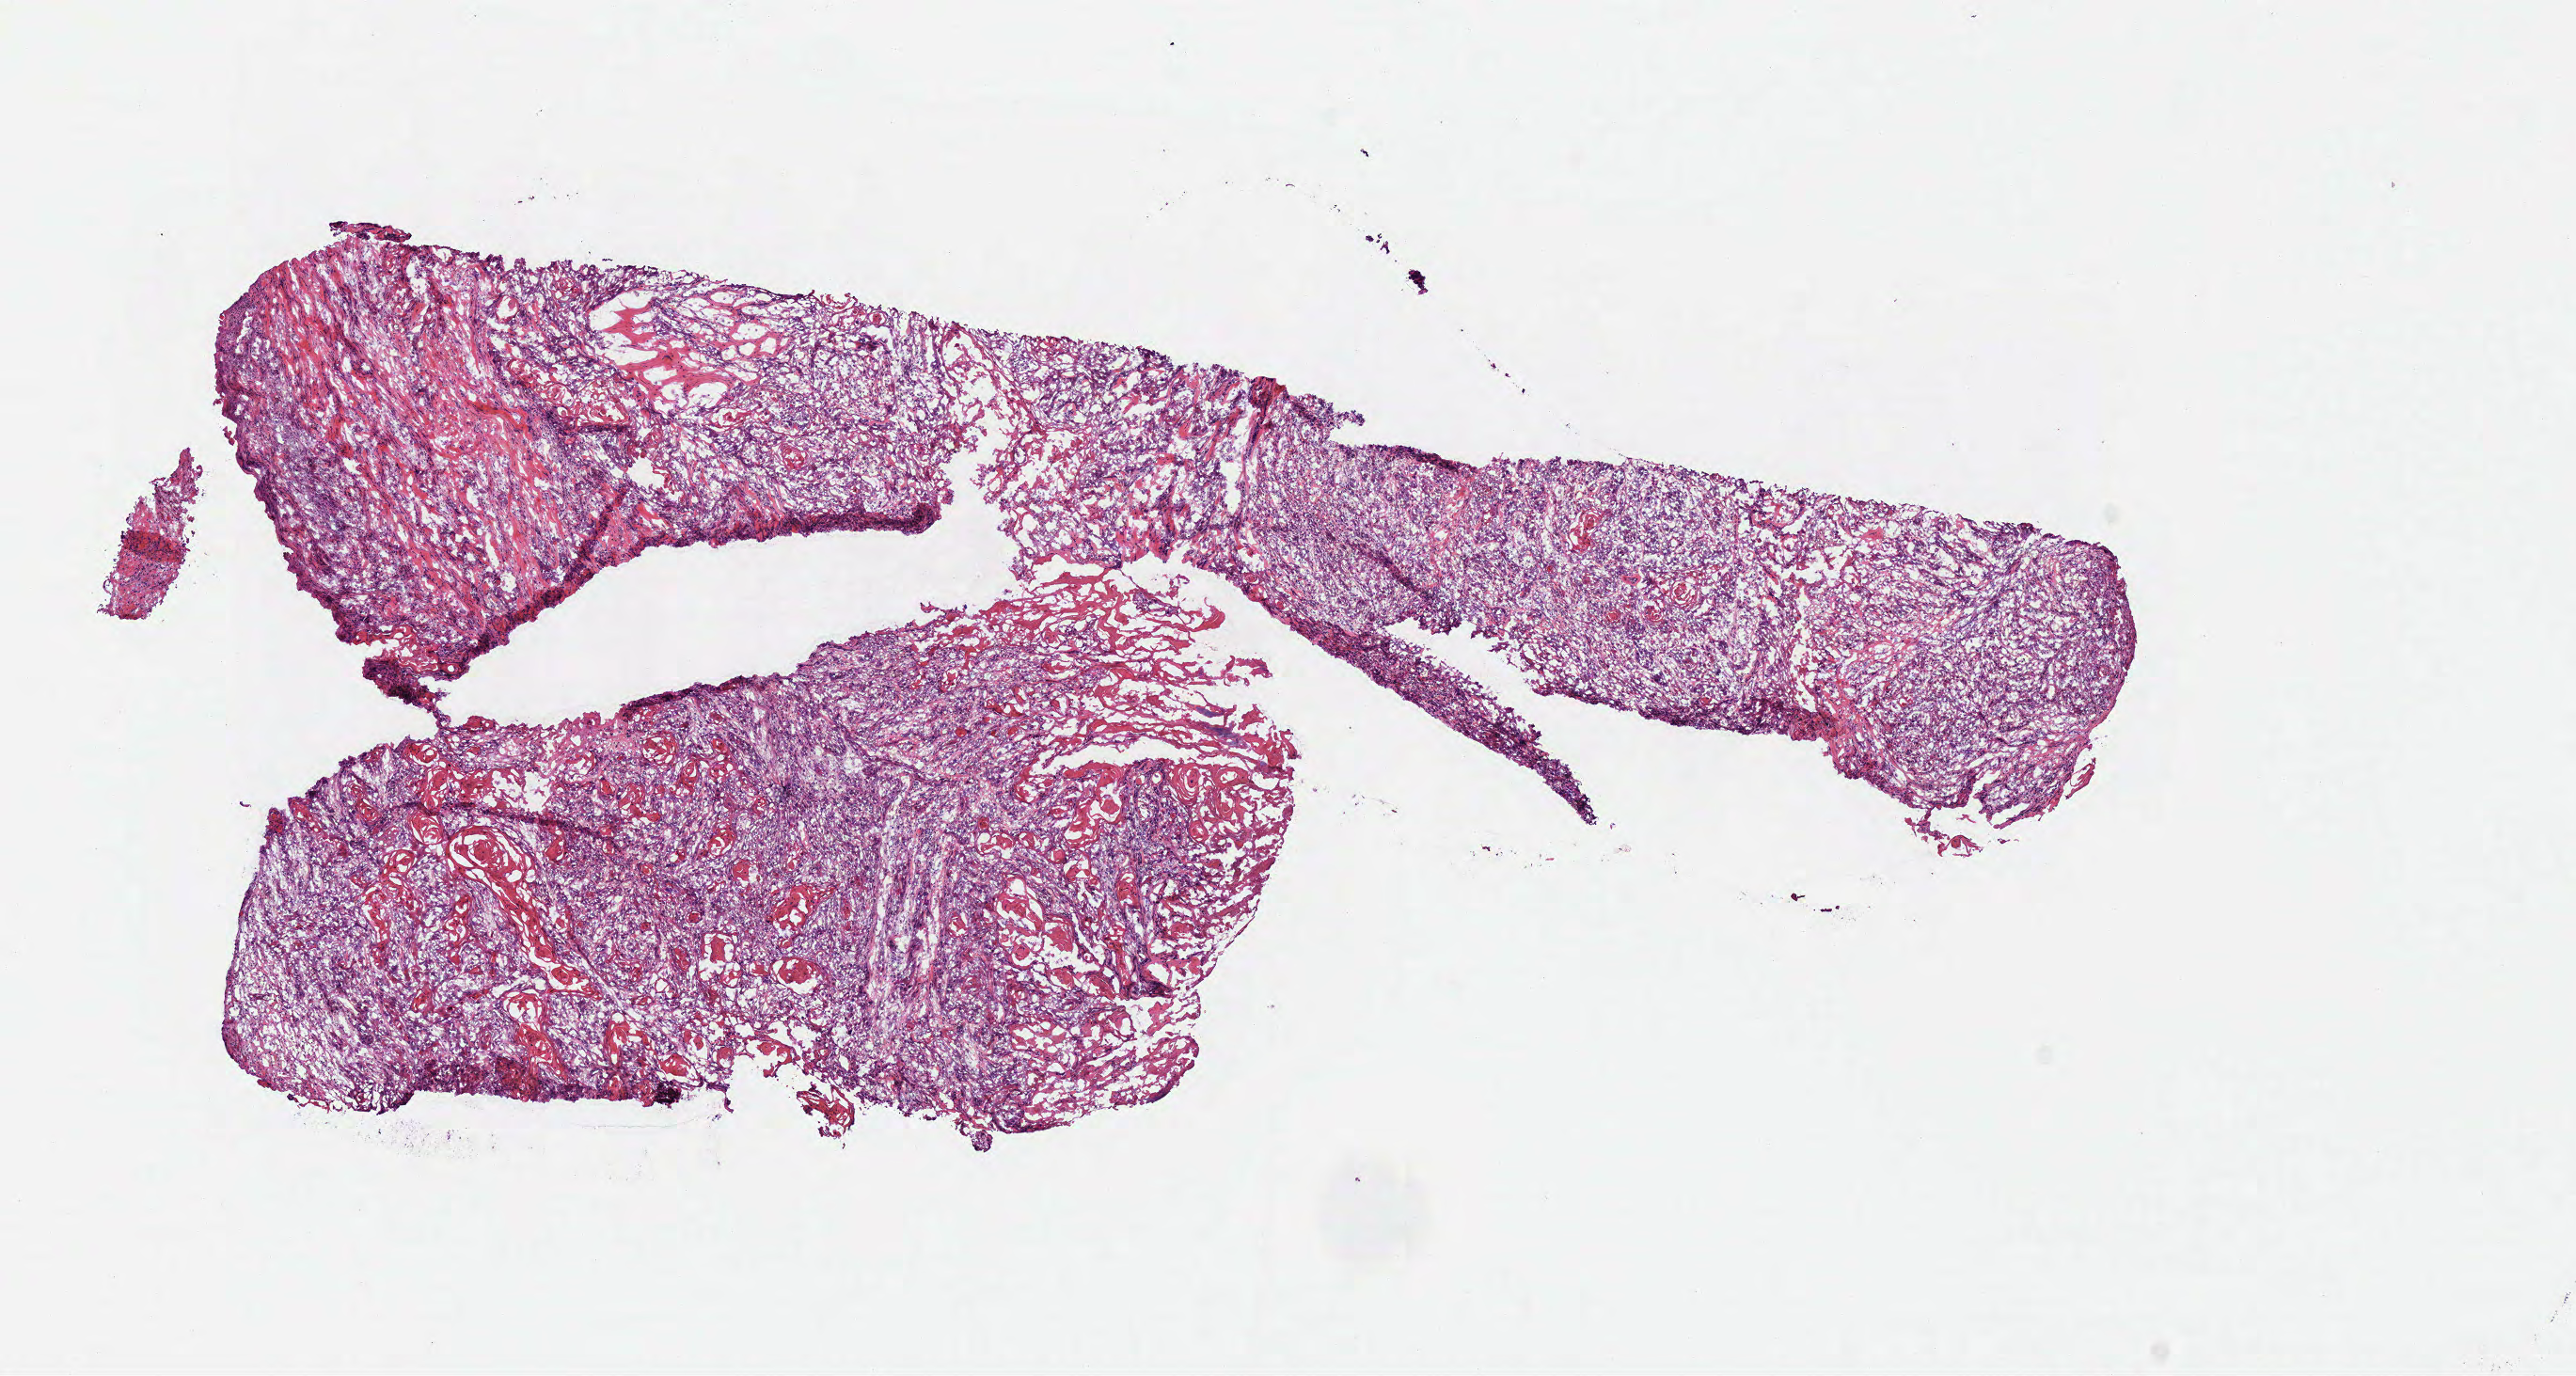
Whole-slide histology image, H&E-stained, whole scanned area (about 10.8 x 5.8 mm) shown as a low-resolution overview, frozen section from the bottom of the tissue portion, head and neck, primary tumour sample. Male patient; age at initial diagnosis 53 years.
Histologic diagnosis: Squamous cell carcinoma, NOS (overlapping lesion of lip, oral cavity and pharynx).